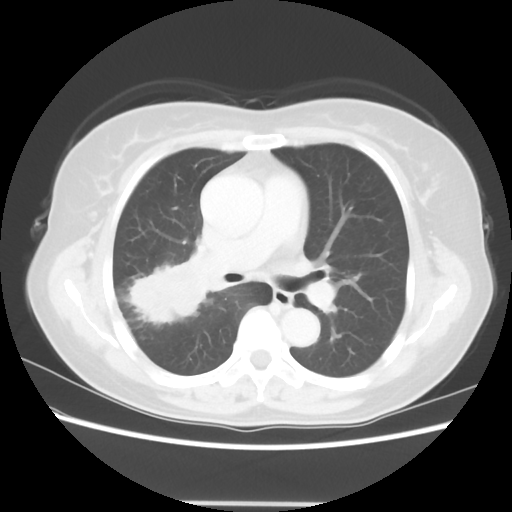
Chest CT, one axial slice. Slice 35 of 56 in the series (ordered by position). 120 kVp. Lung window (W 1500 / L -600 HU). 512 × 512 image matrix, field of view 360 × 360 mm. Female patient, age 55 years. From the clinical record (not read from this slice): clinical TNM (as recorded): T2 N1 M0.
Structures marked on this image (bounding box drawn by a radiologist):
- lung tumour (recorded histology: adenocarcinoma): bounding box [x1, y1, x2, y2] px = [122, 256, 225, 333]